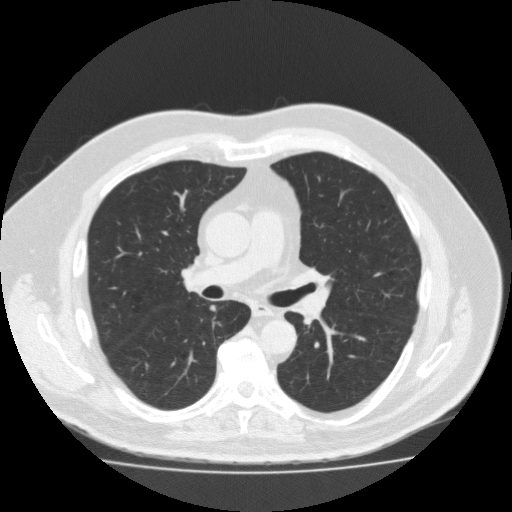
Axial slice from a low-dose chest CT screening exam. Second annual screen. Lung window (W 1500 / L -600 HU). 2 mm slice thickness. Slice 69 of 188 in the series. 512 × 512 image matrix. Male, age 56 years at enrolment.
Expert reader's lesion annotation, bounding box [x1, y1, x2, y2] px = [198, 299, 230, 322]. The exam's reader record, not a measurement of the box and not confirmed to be the same lesion: non-calcified nodule or mass ≥4 mm, right lower lobe, 5 × 5 mm, spiculated (stellate) margins, soft tissue attenuation, pre-existing on the prior screen: no. Later outcome: lung cancer diagnosed 448 days after this screen (after the third annual screen) — adenocarcinoma, NOS, right lower lobe, moderately differentiated (G2), stage IA (AJCC 6th edition), 12 mm at pathology.